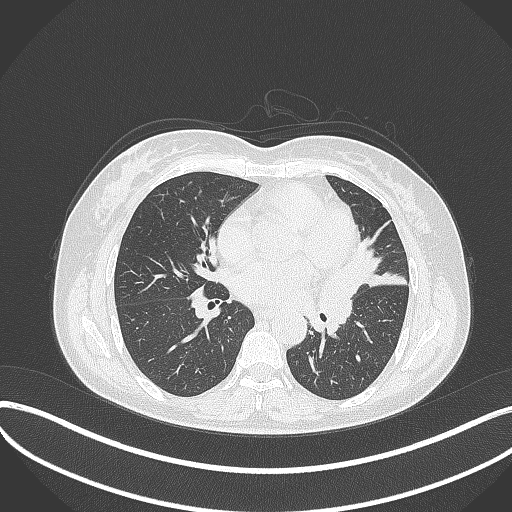
Chest CT, one axial slice. Position 170 of 373 along the scan axis. Lung window (W 1500 / L -600 HU). 1 mm slice thickness. 512 × 512 image matrix. Patient: female, 54 years. Case-level facts recorded for this patient, not image findings: clinical TNM (as recorded): T2a N1 M0; histopathological grade: G3.
Annotated regions visible in this slice (rectangle marked by the reading radiologist):
- lung tumour (recorded histology: small cell carcinoma): bounding box <319,261,365,328> (left, top, right, bottom; pixels)